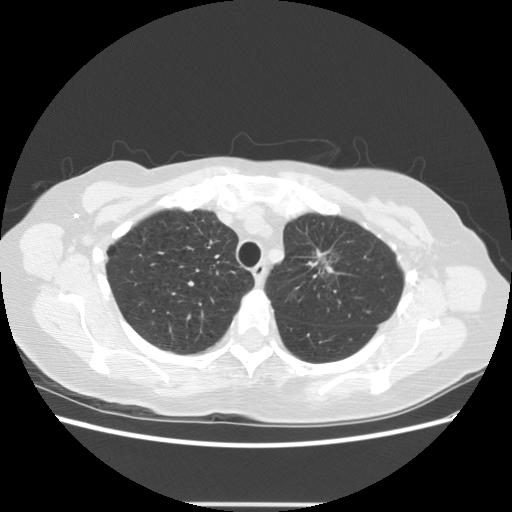
Chest CT (low-dose screening protocol), one axial image, third screening round (two years after baseline), lung window (W 1500 / L -600 HU), standard (soft-tissue) reconstruction kernel (STANDARD), 512 × 512 image matrix. Female, age 65 years at enrolment. Former smoker at enrolment.
Lesion marked by an expert reader, bounding box (x1, y1, x2, y2) in pixels: (291, 225, 369, 294). The exam's reader record, not a measurement of the box and not confirmed to be the same lesion: non-calcified nodule or mass ≥4 mm, left upper lobe, 17 × 14 mm, poorly defined margins, ground glass attenuation, pre-existing on the prior screen: yes; interval growth: yes. Lung cancer was diagnosed 96 days after this screen: adenocarcinoma, NOS, left upper lobe, moderately differentiated (G2), stage IA (AJCC 6th edition), 30 mm at pathology.